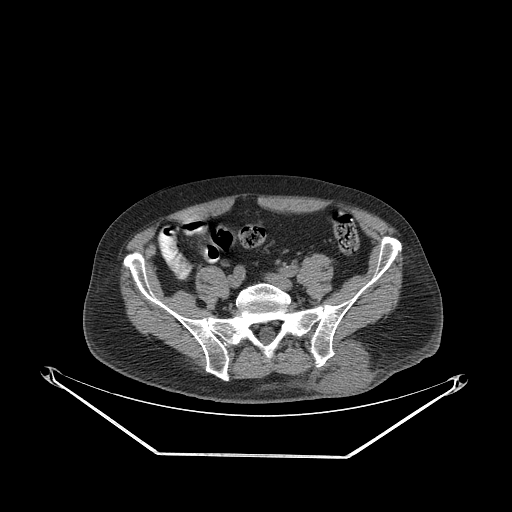
CT of an extremity soft-tissue mass (from a PET/CT study), one axial slice; position 81 of 267 along the scan axis; reconstruction kernel STANDARD; 140 kVp; soft-tissue window (W 400 / L 40 HU); 3.75 mm slice thickness; 512 × 512 image matrix. Male patient. From the clinical record (not read from this slice): histological type: leiomyosarcoma; grade: intermediate; site of the primary tumour: left pelvis.
Structures marked on this image (expert contour drawn on MRI and transferred to this co-registered scan by the dataset authors):
- gross tumour volume (mass): bounding box [x1, y1, x2, y2] px = [311, 340, 373, 396]